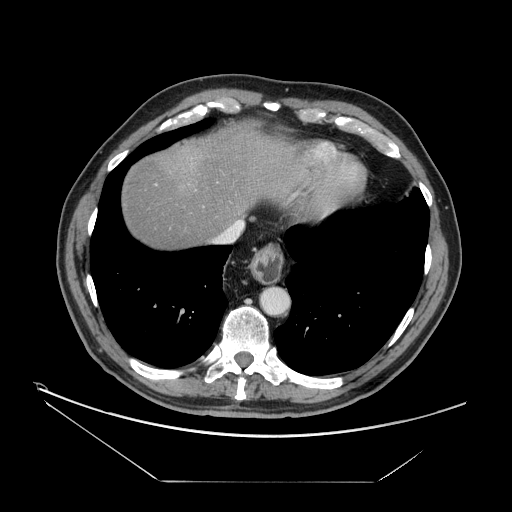
Contrast-enhanced abdominal CT, one axial slice; position 143 of 161 along the scan axis; 120 kVp; intravenous contrast given; soft-tissue window (W 400 / L 40 HU); 2.5 mm slice thickness; 512 × 512 image matrix, field of view 440 × 440 mm. Male patient, age 65 years. Case-level facts recorded for this patient, not image findings: diagnosis: colorectal cancer liver metastases, imaged before liver resection; multiple liver metastases: yes; largest metastasis: 4.2 cm; disease in both lobes: yes.
Structures marked on this image (manually delineated by an expert):
- hepatic veins: box from (x=217, y=220) to (x=244, y=243) px
- liver: (x=121, y=125)–(x=299, y=249)
- planned liver remnant (the part of the liver to remain after resection): (x=121, y=125)–(x=299, y=249)